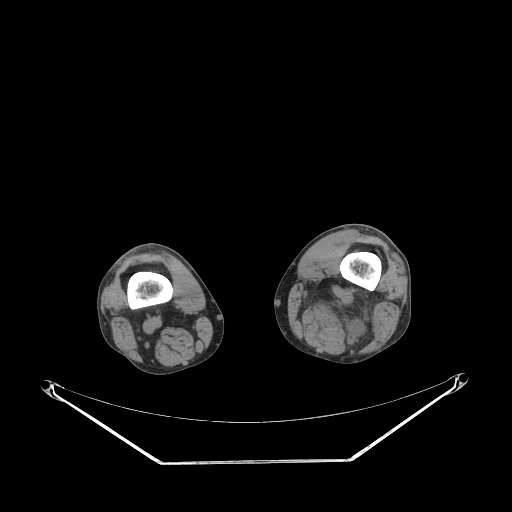
CT of an extremity soft-tissue mass (from a PET/CT study), one axial slice. Reconstruction kernel STANDARD. Soft-tissue window (W 400 / L 40 HU). 512 × 512 image matrix, field of view 500 × 500 mm. Male patient. Case-level facts recorded for this patient, not image findings: histological type: undifferentiated pleomorphic liposarcoma; grade: high; site of the primary tumour: left thigh.
Annotated regions visible in this slice (expert contour drawn on MRI and transferred to this co-registered scan by the dataset authors):
- gross tumour volume including surrounding oedema: bounding box (x1, y1, x2, y2) in pixels: (295, 278, 380, 346)